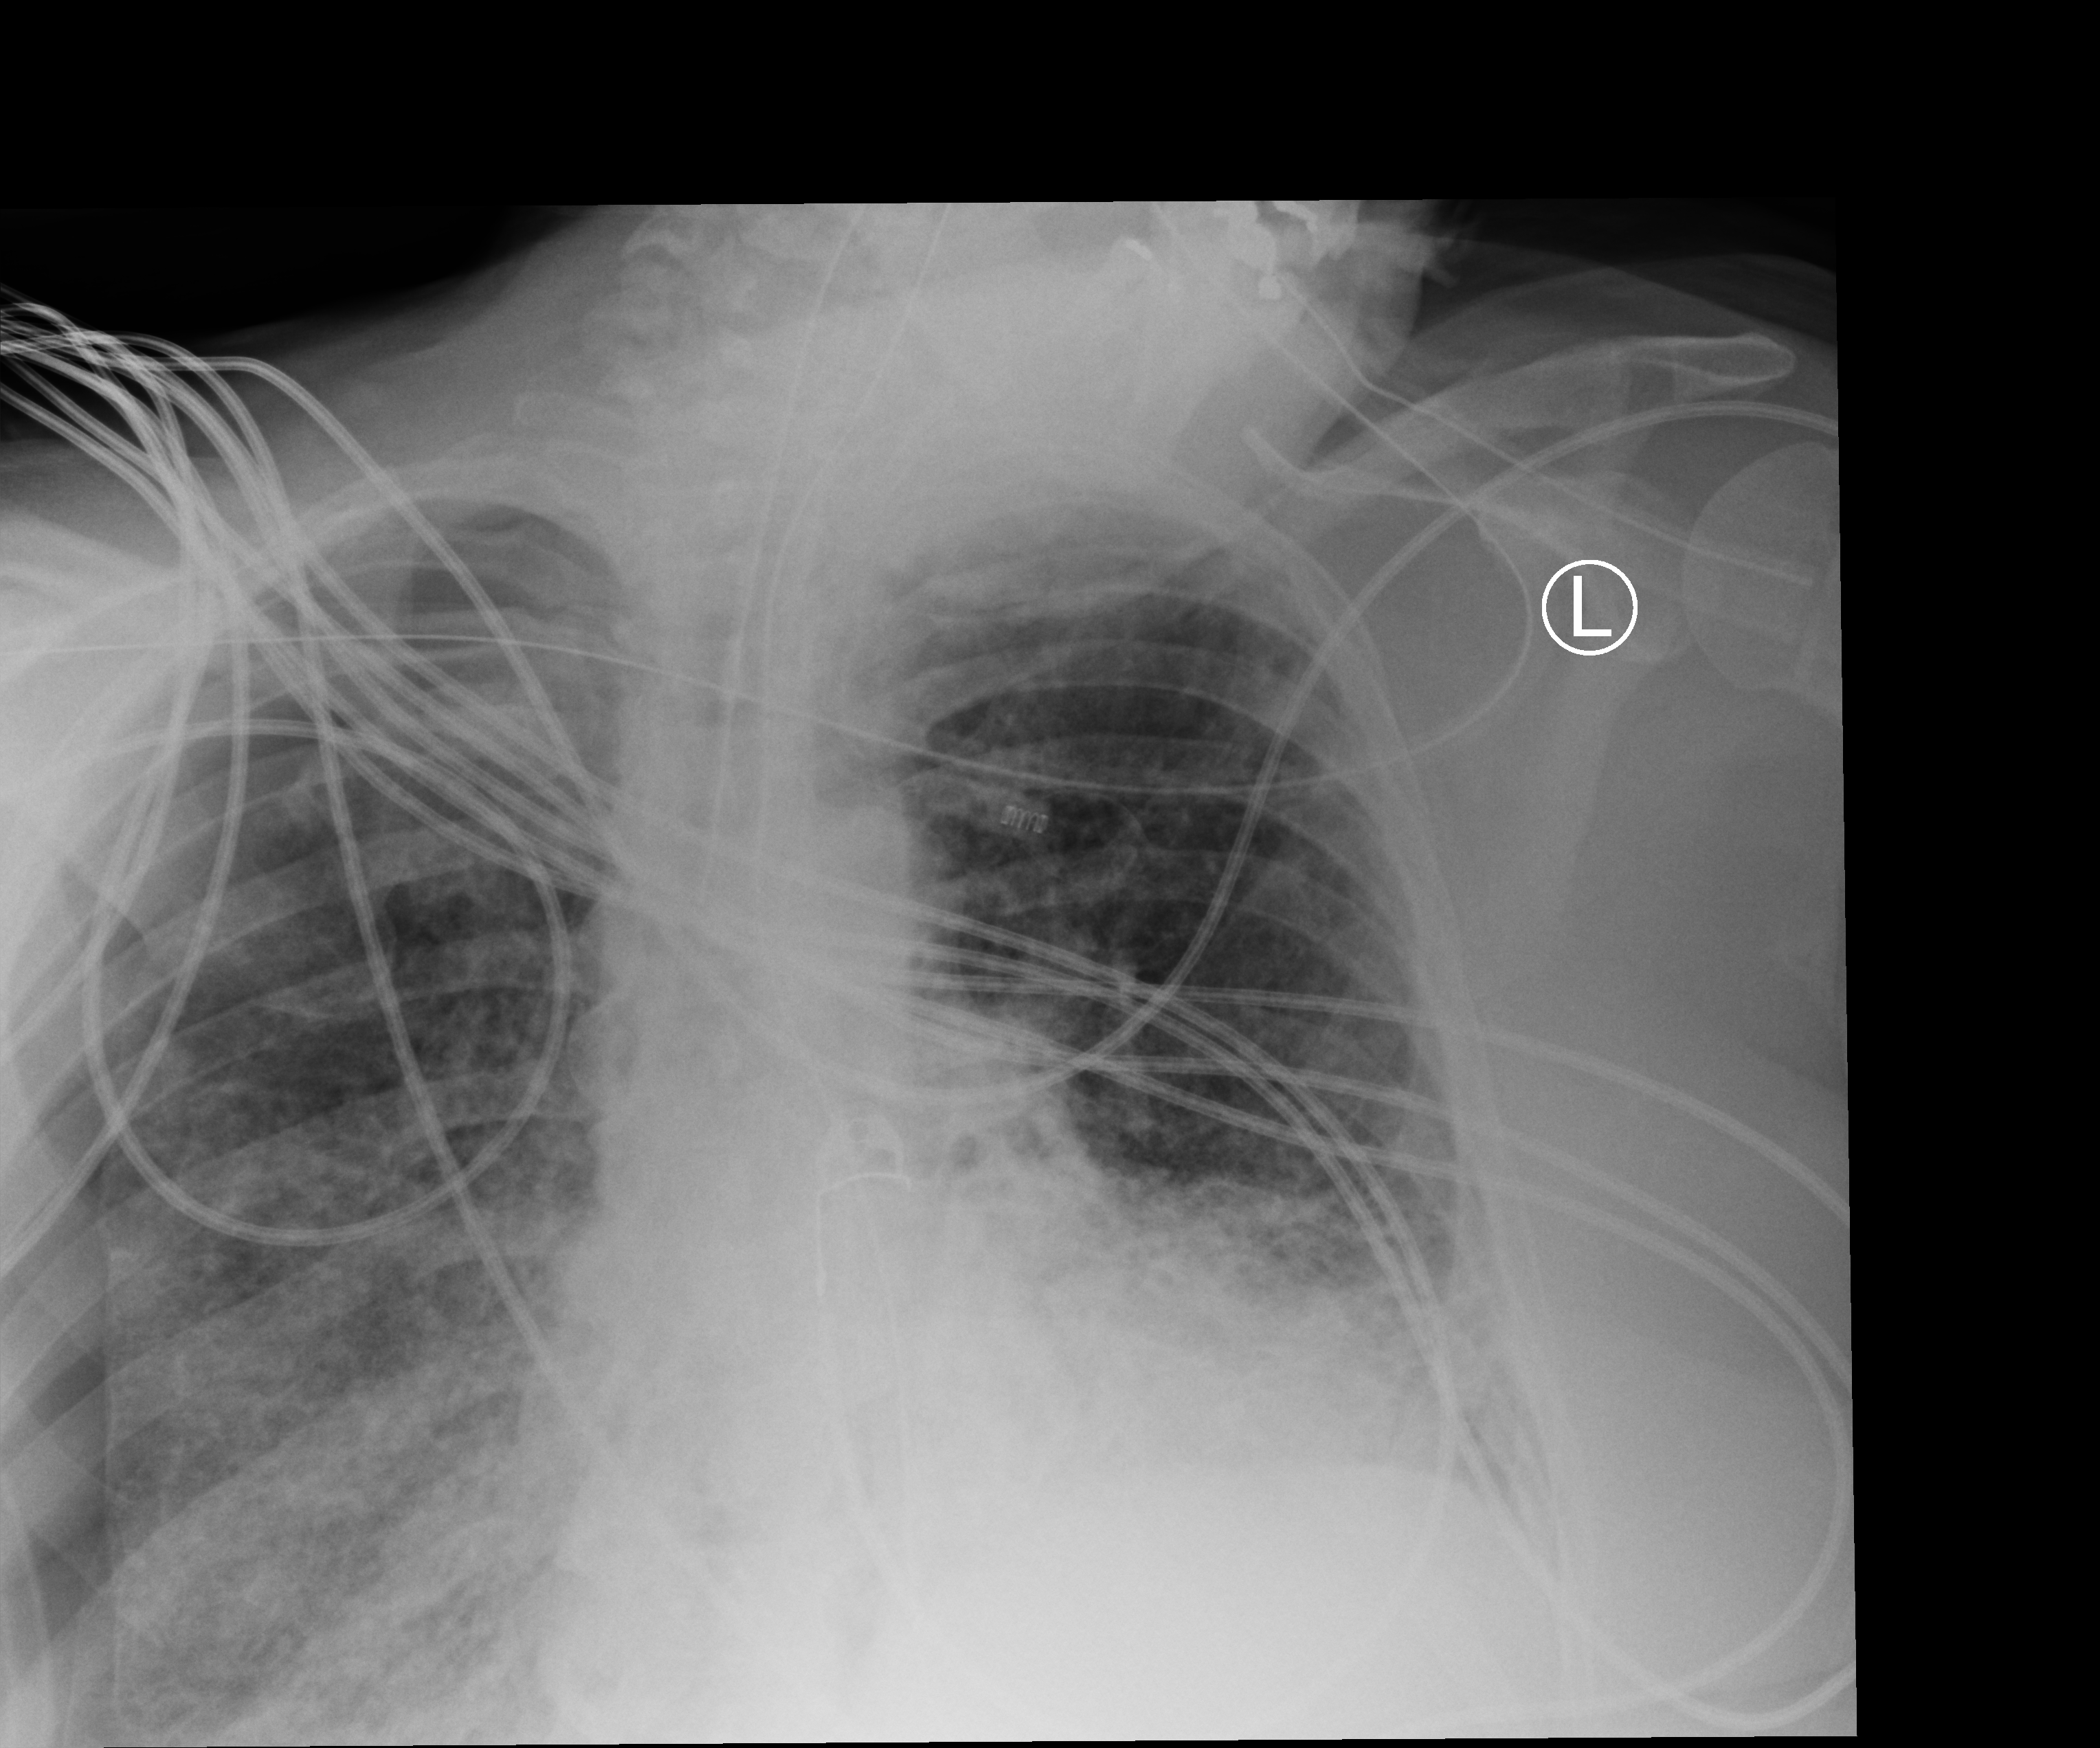
Bedside chest radiograph (computed radiography), anteroposterior (AP) projection. Patient hospitalised with COVID-19, aged 18–59 years.
Hospital-stay facts (about this admission, not read from this image; timing relative to this image not recorded):
- length of hospital stay: 28 days